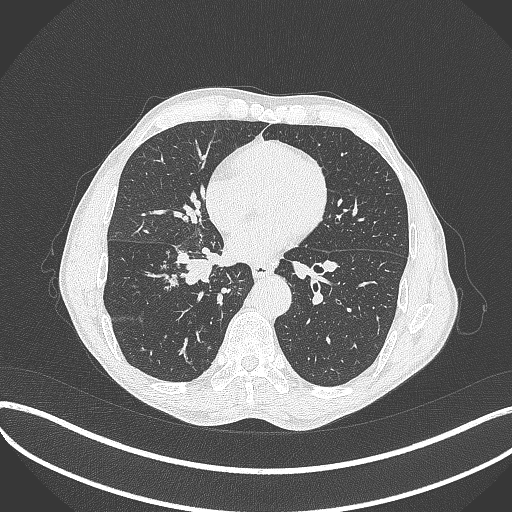
Chest CT, one axial slice; slice 187 of 481 in the series (ordered by position); 120 kVp; lung window (W 1500 / L -600 HU); 512 × 512 image matrix. Patient: male, 65 years. Case-level facts recorded for this patient, not image findings: clinical TNM (as recorded): T2a N0 M0; histopathological grade: G2.
Annotated regions visible in this slice (rectangle marked by the reading radiologist):
- lung tumour (recorded histology: squamous cell carcinoma): box from (x=165, y=243) to (x=224, y=285) px